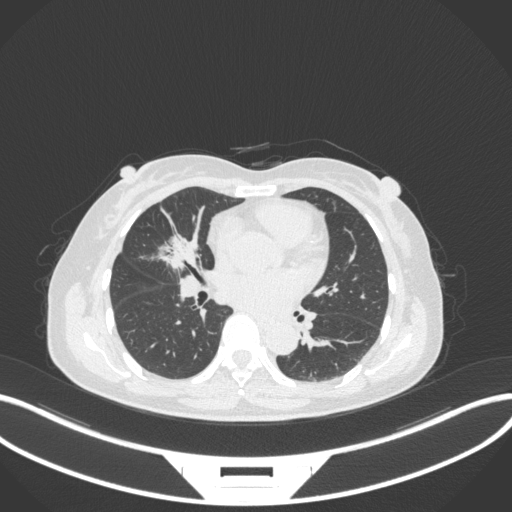
Chest CT, one axial slice; position 147 of 282 along the scan axis; reconstruction kernel B31f; 120 kVp; lung window (W 1500 / L -600 HU); 1 mm slice thickness; 512 × 512 image matrix, field of view 400 × 400 mm. Patient: female, 51 years. Case-level facts recorded for this patient, not image findings: clinical TNM (as recorded): T1c N0 M0; histopathological grade: G2.
Outlined on this slice (rectangle marked by the reading radiologist):
- lung tumour (recorded histology: adenocarcinoma): bounding box [x1, y1, x2, y2] px = [155, 225, 203, 269]